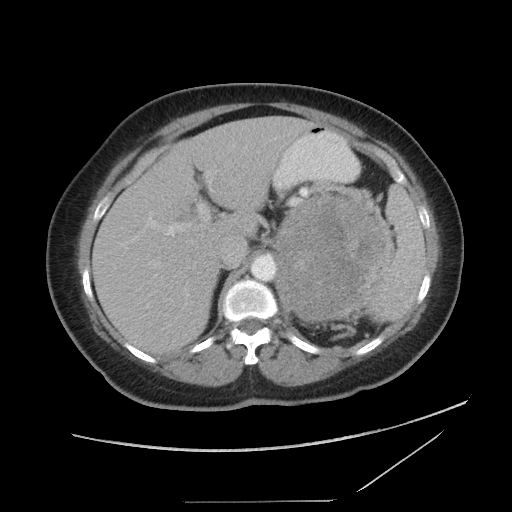
Contrast-enhanced abdominal CT, one axial slice. Slice 62 of 86 in the series (ordered by position). Intravenous contrast given. Soft-tissue window (W 400 / L 40 HU). 5 mm slice thickness. 512 × 512 image matrix, field of view 398 × 398 mm. Patient: female, 77 years. Case-level facts recorded for this patient, not image findings: diagnosis: adrenocortical carcinoma; tumour side: left adrenal; tumour size at pathology: 13.1 cm; Ki-67 index: 10 %; stage (as recorded): 3.
Annotated regions visible in this slice (semi-automatic segmentation, software-assisted and operator-edited):
- mass: box from (x=276, y=196) to (x=394, y=320) px